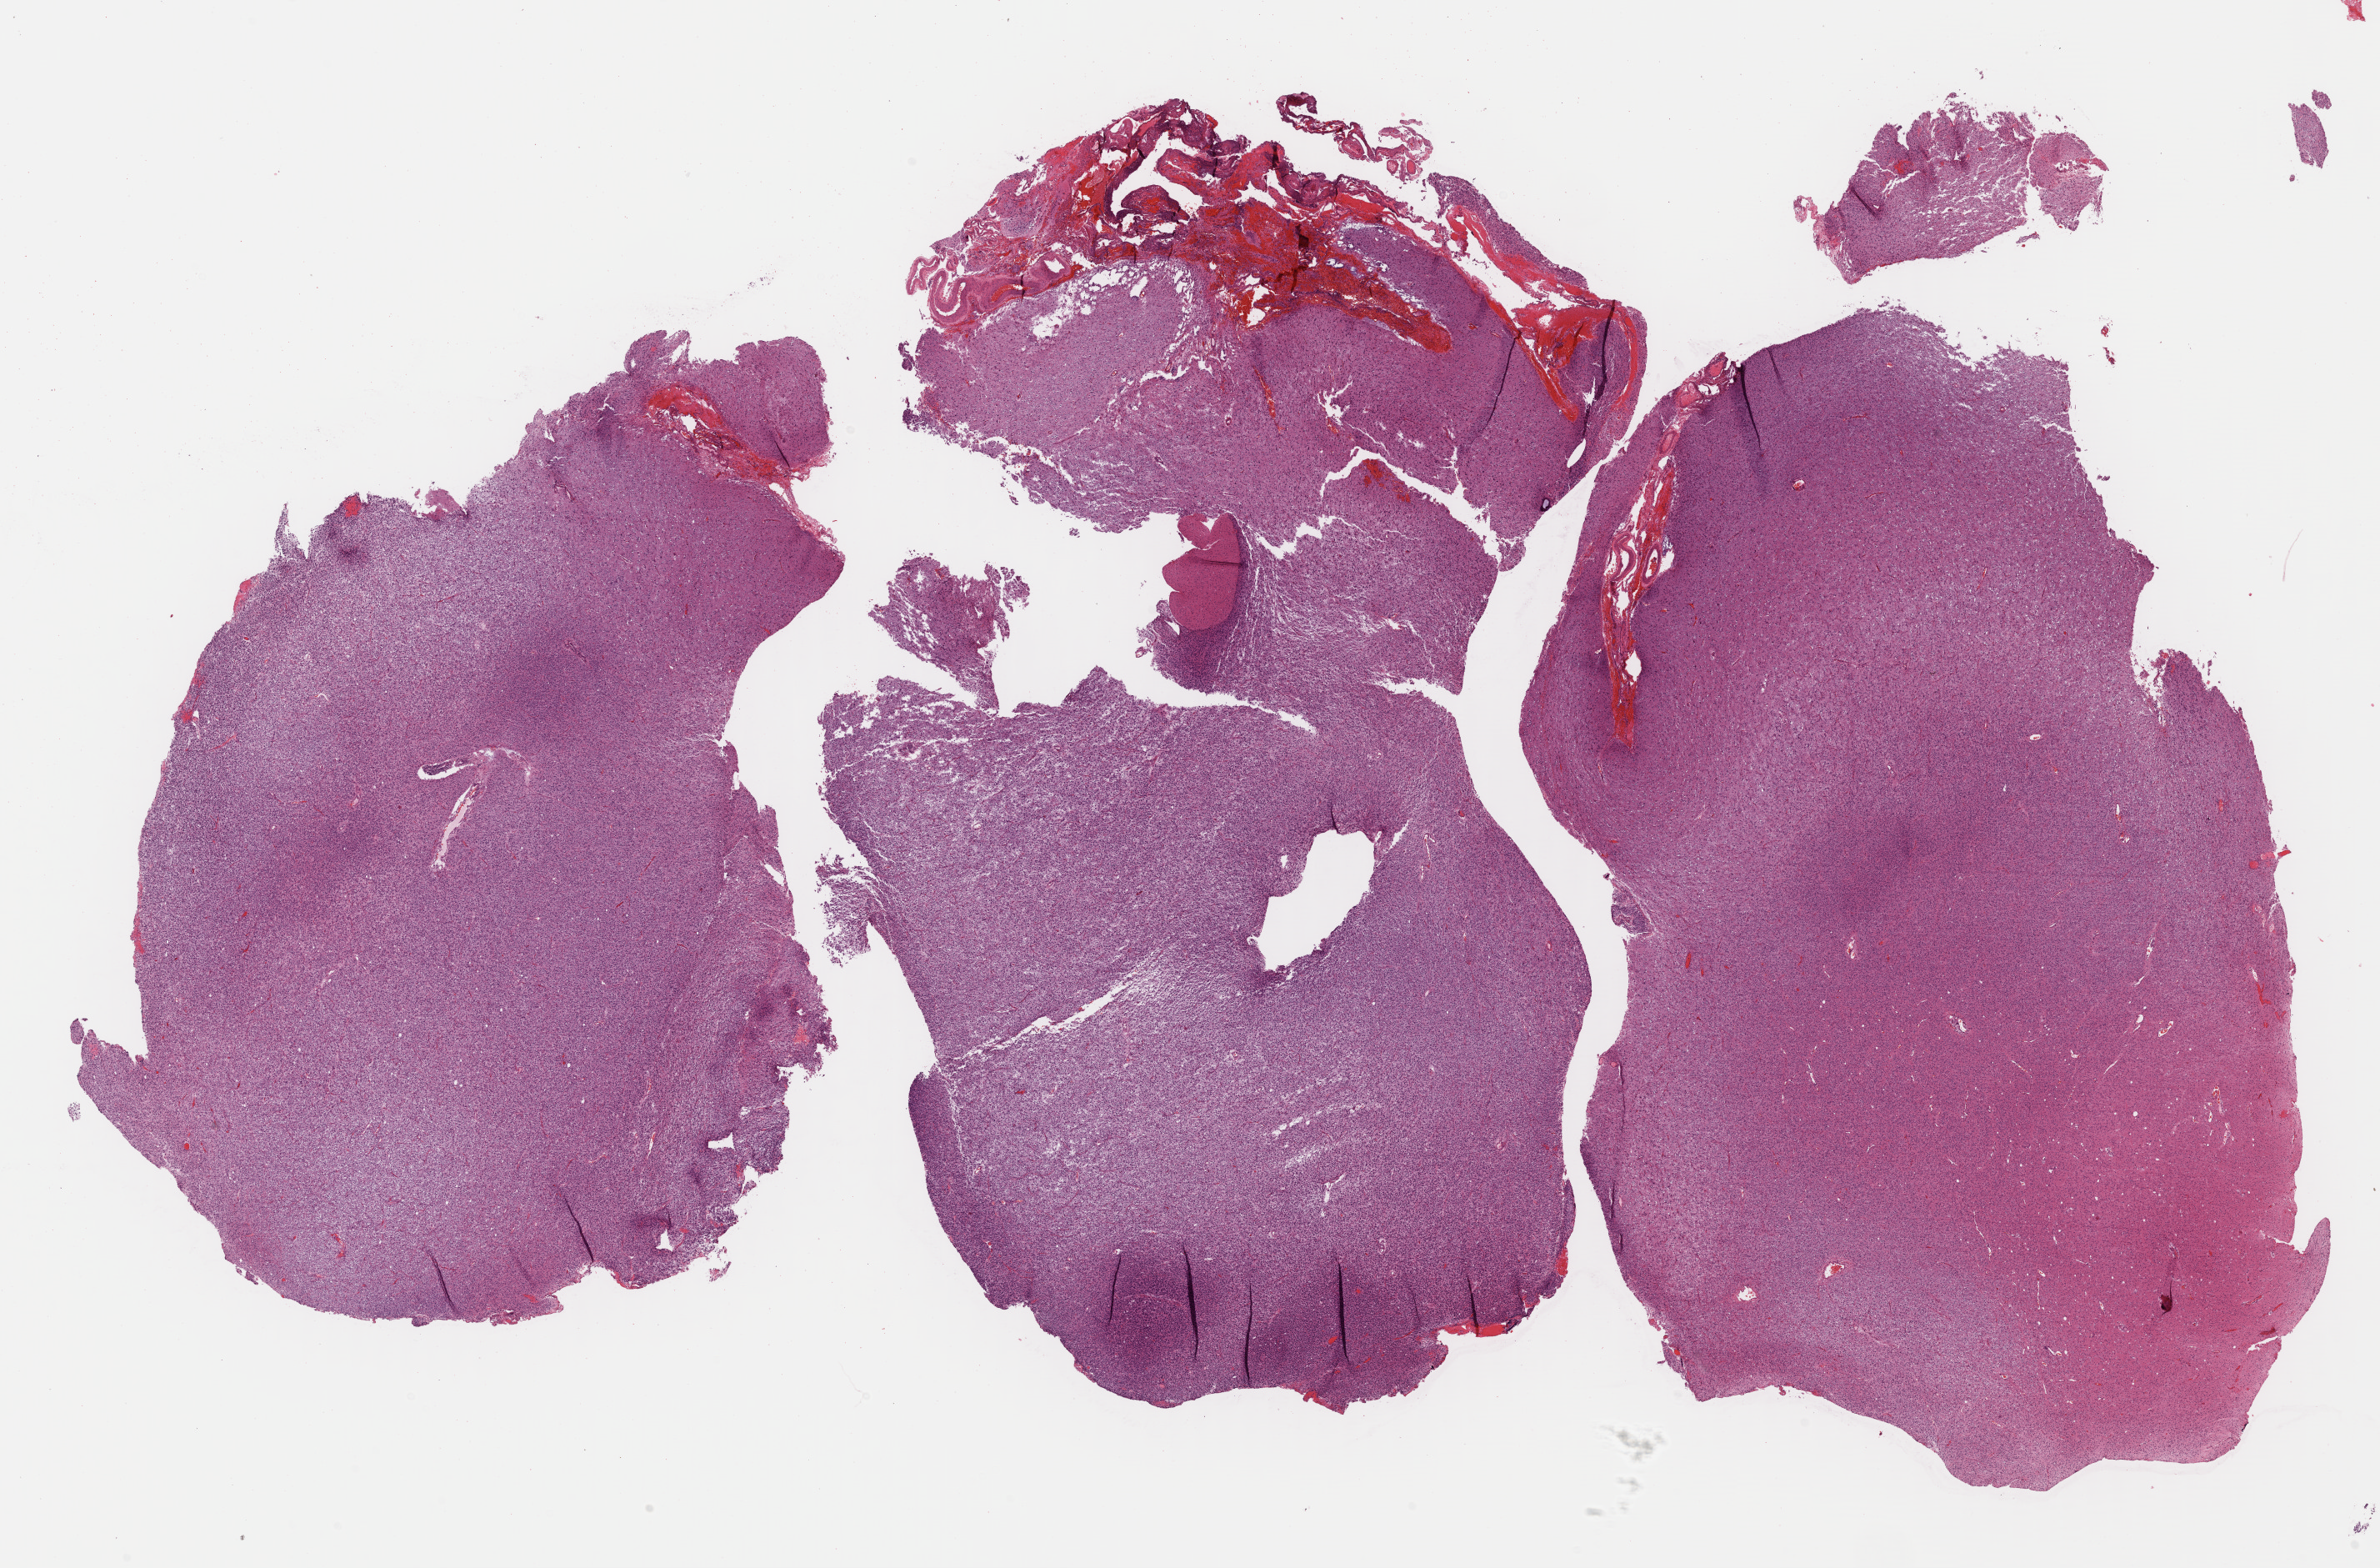
Digitized Hematoxylin and eosin (H&E) stained tissue section (whole slide), whole scanned area (about 22.4 x 14.8 mm, acquisition: 40x scan) shown as a low-resolution overview; formalin-fixed paraffin-embedded (FFPE) diagnostic section; sample: primary tumour, brain. Male, age 30 years at initial diagnosis. Histologic grade: G3 (poorly differentiated).
Histologic diagnosis: Oligodendroglioma, anaplastic (cerebrum).